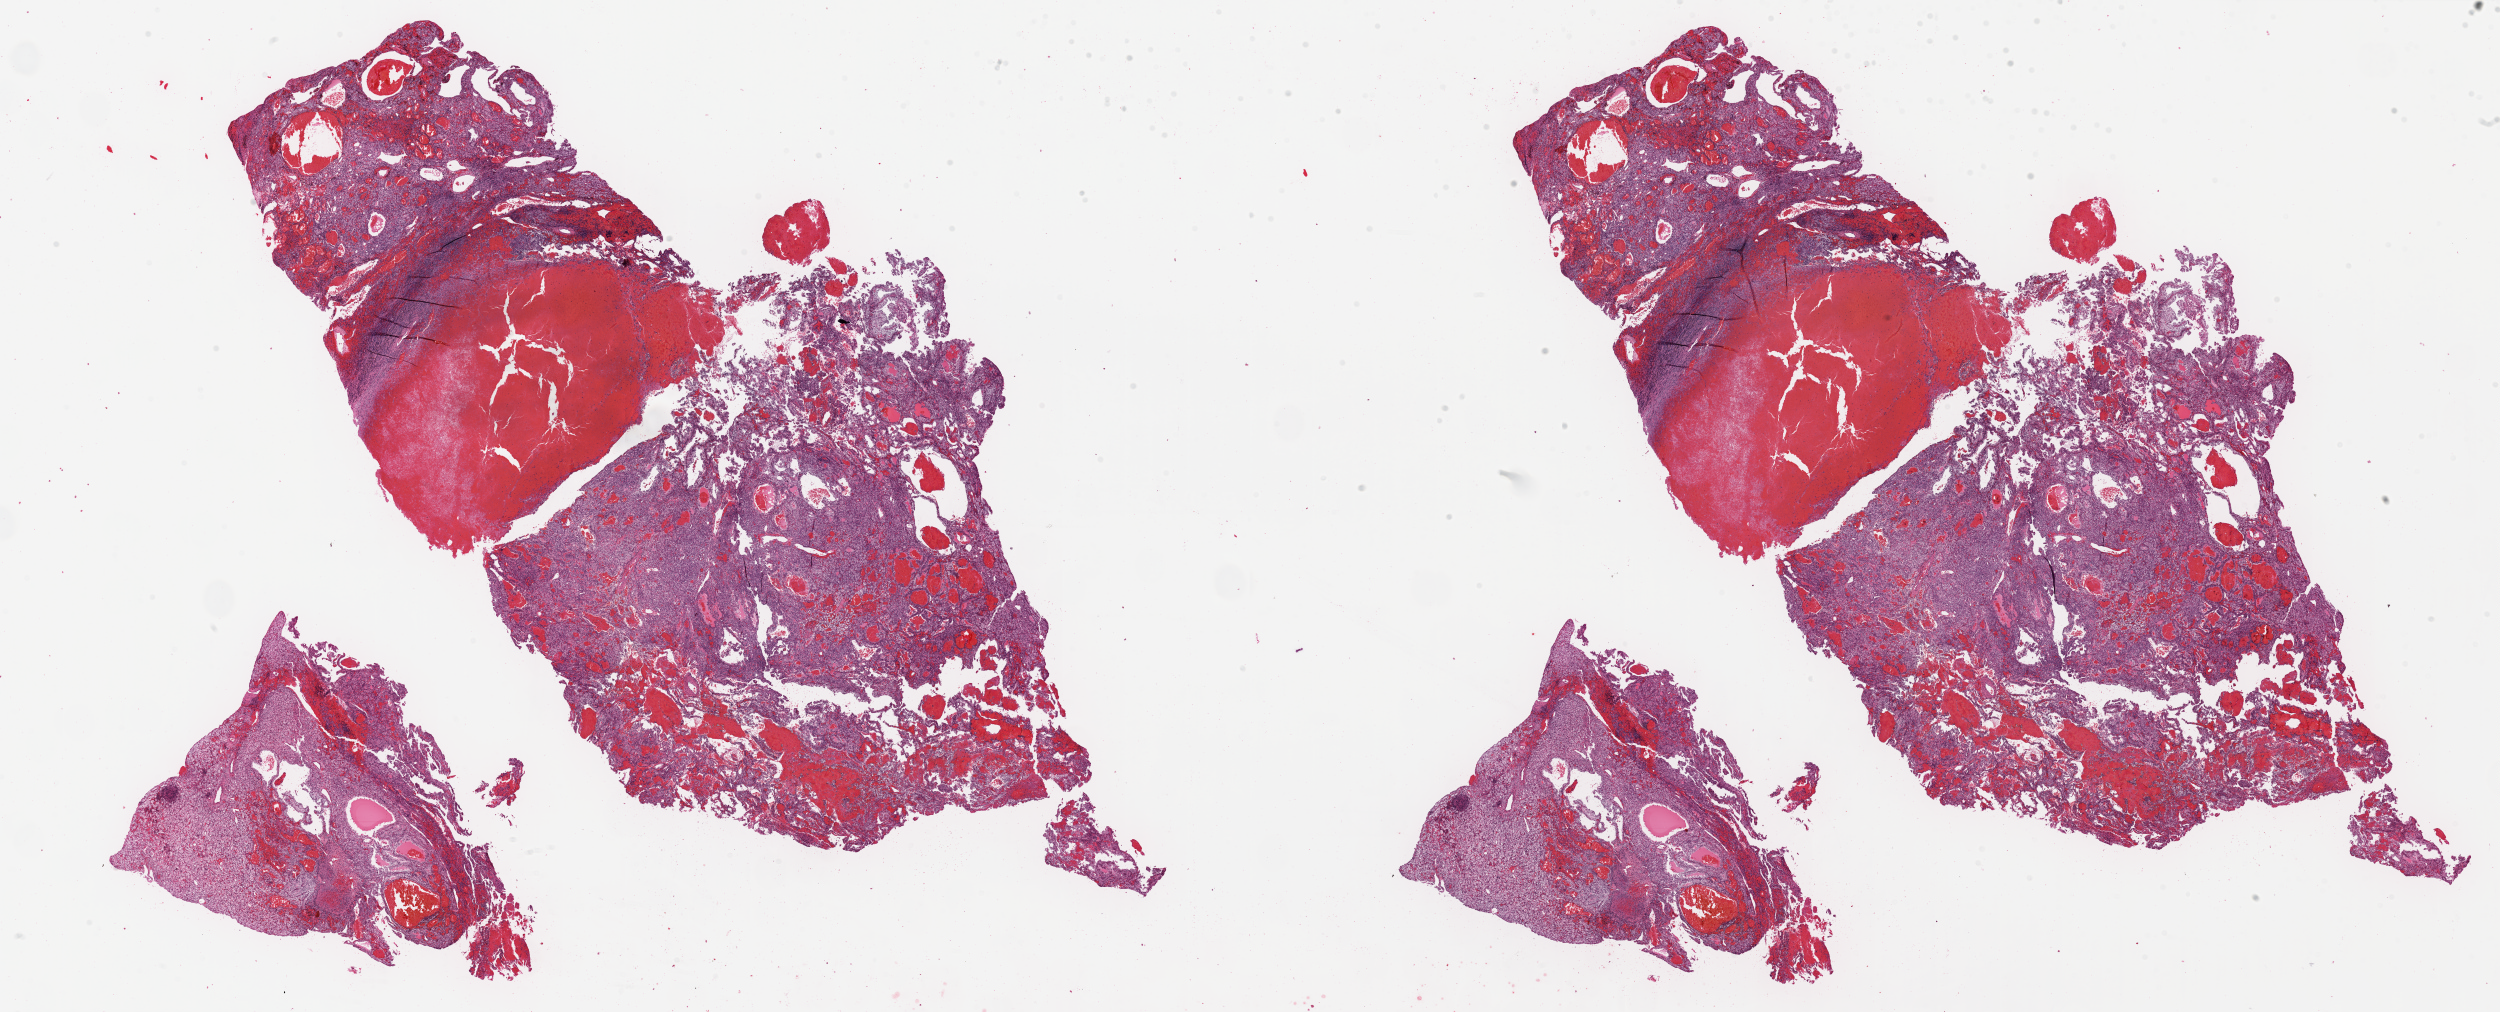
Whole-slide histology image, H&E — low-resolution overview of the scanned area, about 39.5 x 16.0 mm, formalin-fixed paraffin-embedded (FFPE) diagnostic section, sample: primary tumour, kidney. Male patient; age at initial diagnosis 62 years. Histologic grade: G2 (moderately differentiated).
AJCC pathologic stage: II (7th edition). Laterality: left. Diagnosis: Clear cell adenocarcinoma, NOS.